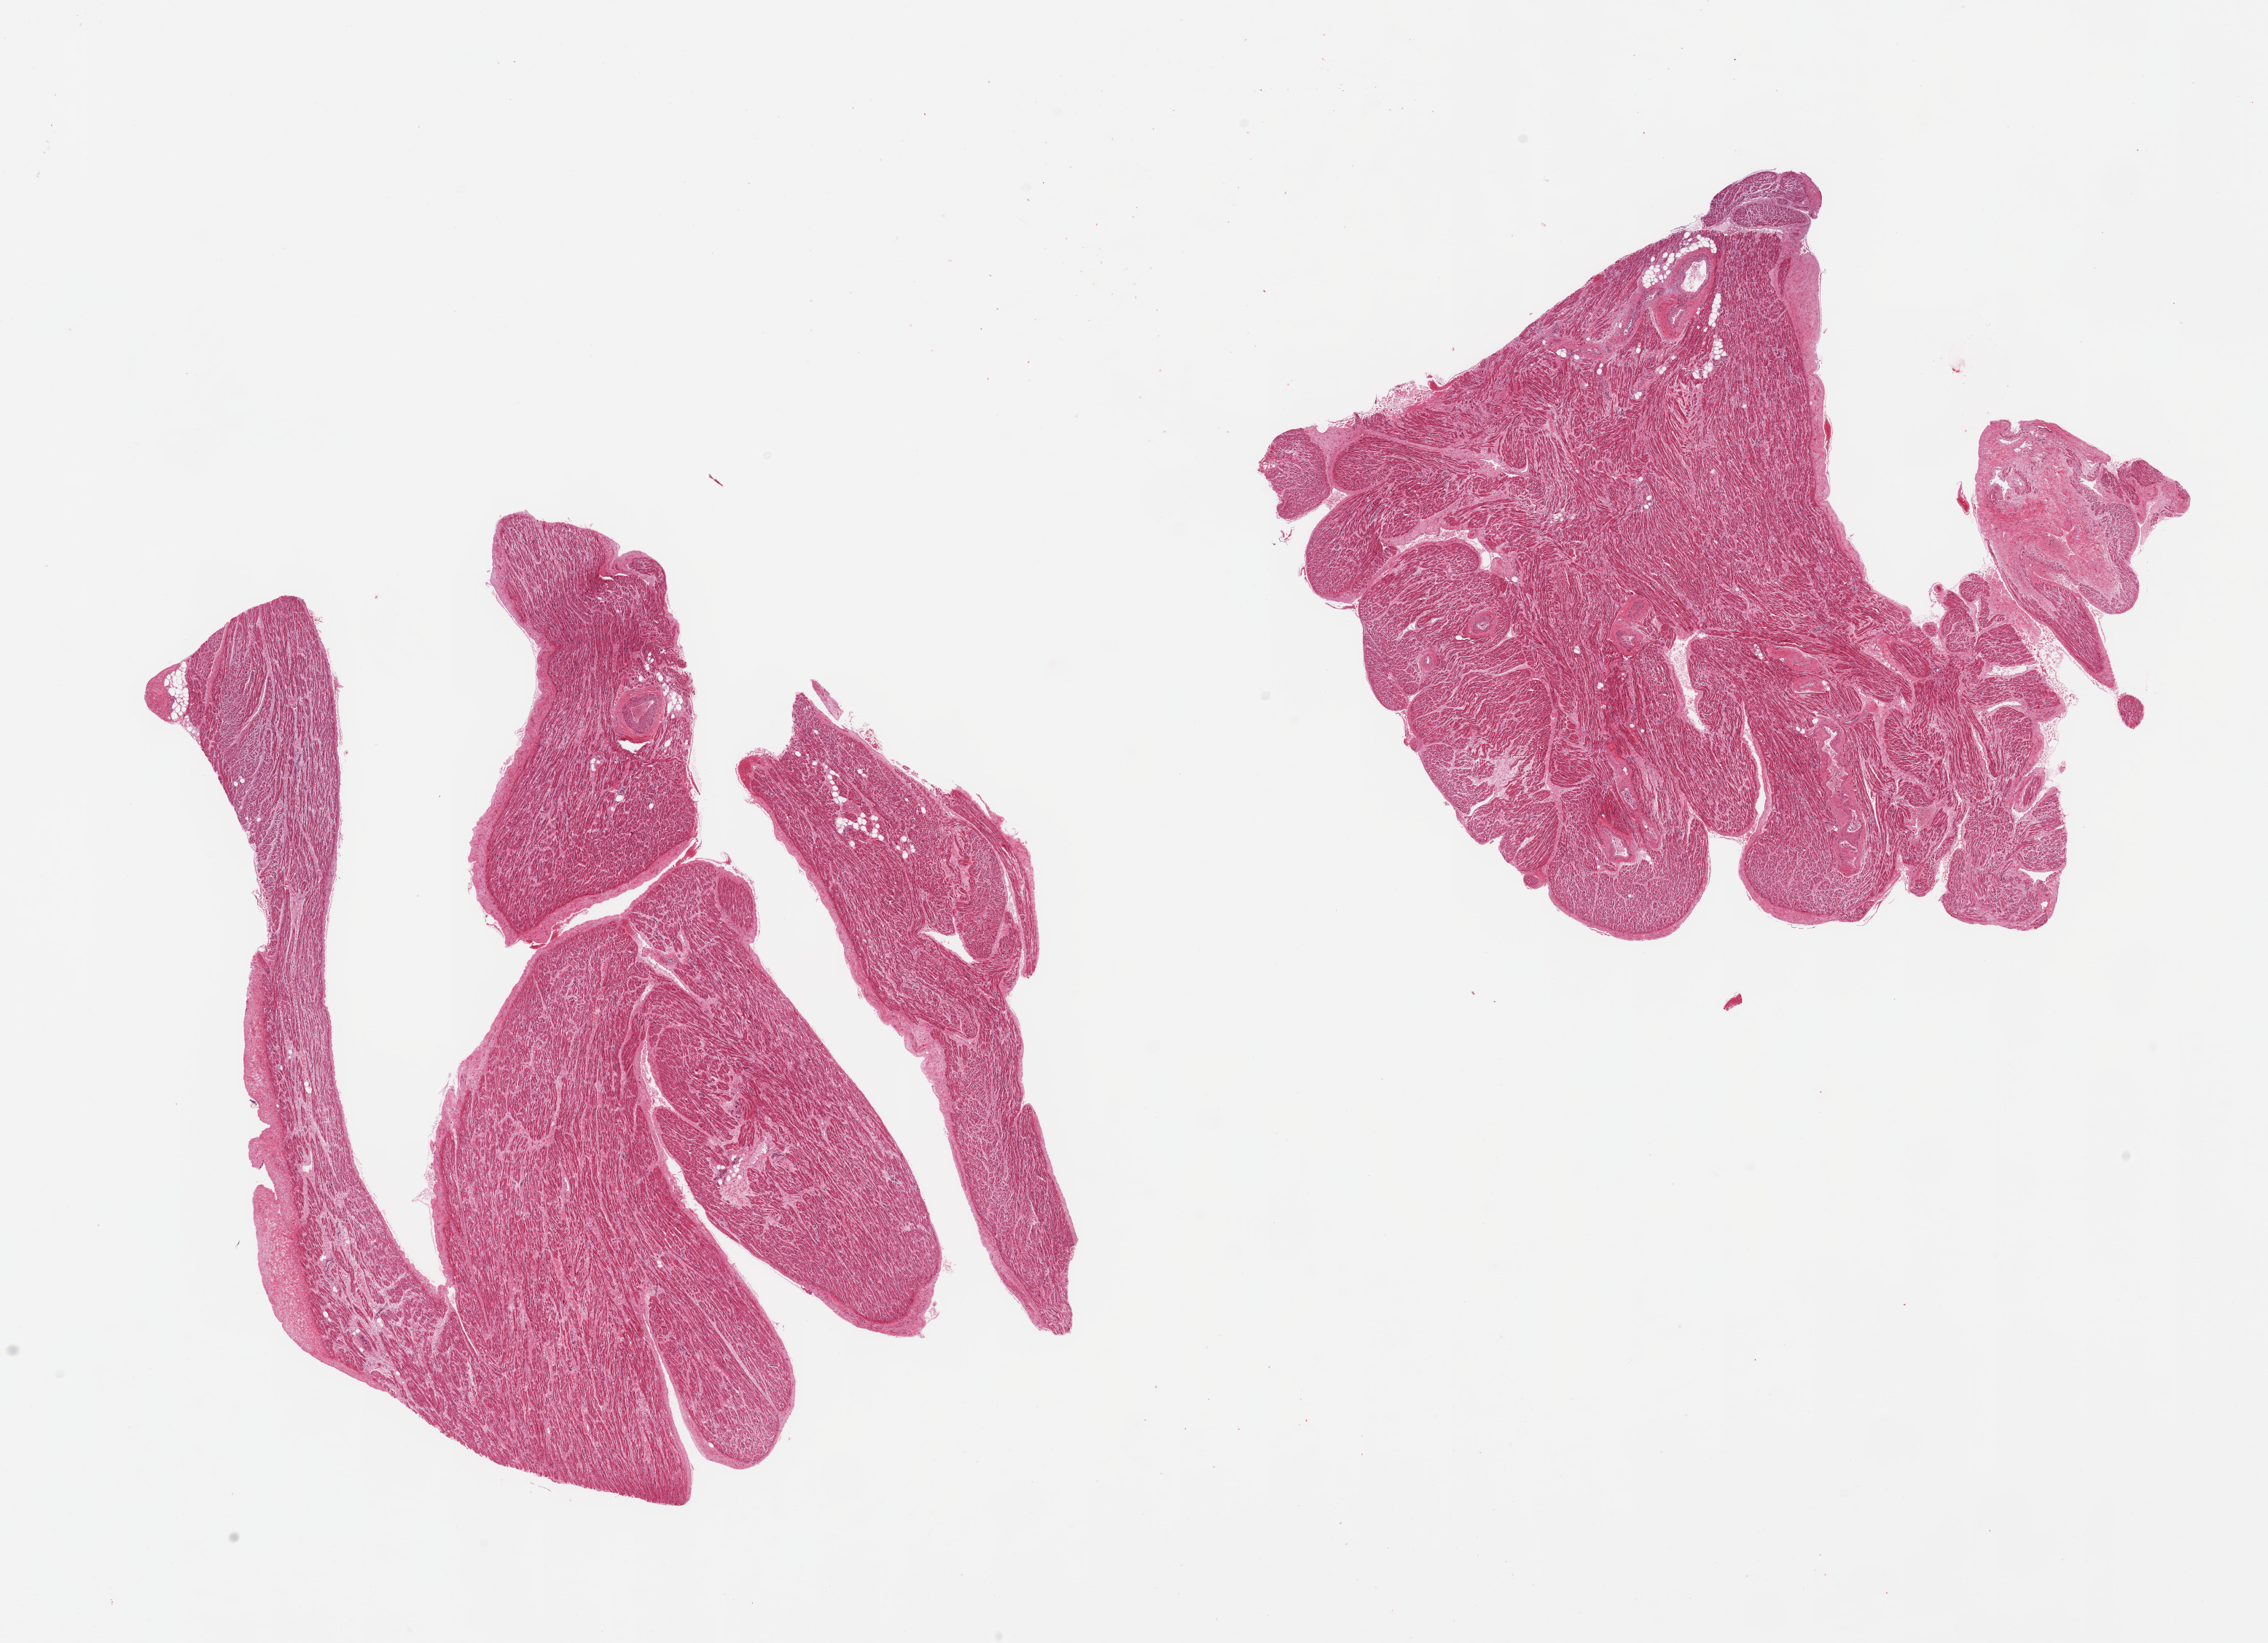
Digitized haematoxylin and eosin-stained section, whole scanned area (about 24.6 x 17.8 mm) shown as a low-resolution overview; PAXgene-fixed paraffin-embedded (PFPE) section; sampled site (target tissue): auricular appendage; tissue donor sample. Donor sex: female.
Review note (as recorded): 2 pieces.